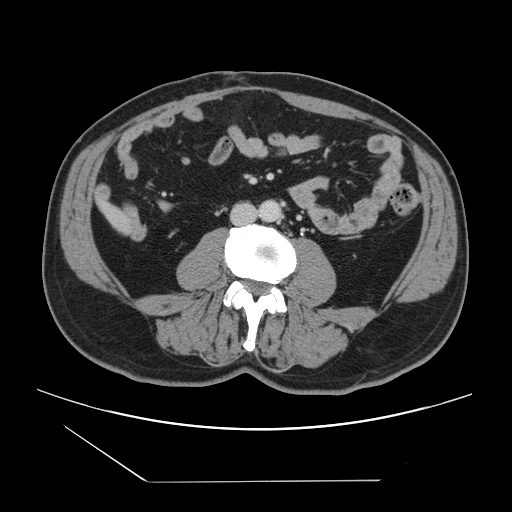
Contrast-enhanced abdominal CT, one axial slice; slice 12 of 157 in the series (ordered by position); intravenous contrast given; soft-tissue window (W 400 / L 40 HU); 2.5 mm slice thickness; 512 × 512 image matrix, field of view 407 × 407 mm. Male patient, age 61 years. Case-level facts recorded for this patient, not image findings: diagnosis: colorectal cancer liver metastases, imaged before liver resection; multiple liver metastases: yes; largest metastasis: 5.5 cm; chemotherapy before resection: no.
Outlined on this slice (outlined manually by an expert reader):
- liver: bounding box <102,204,127,232> (left, top, right, bottom; pixels)
- planned liver remnant (the part of the liver to remain after resection): <102,203,118,216>